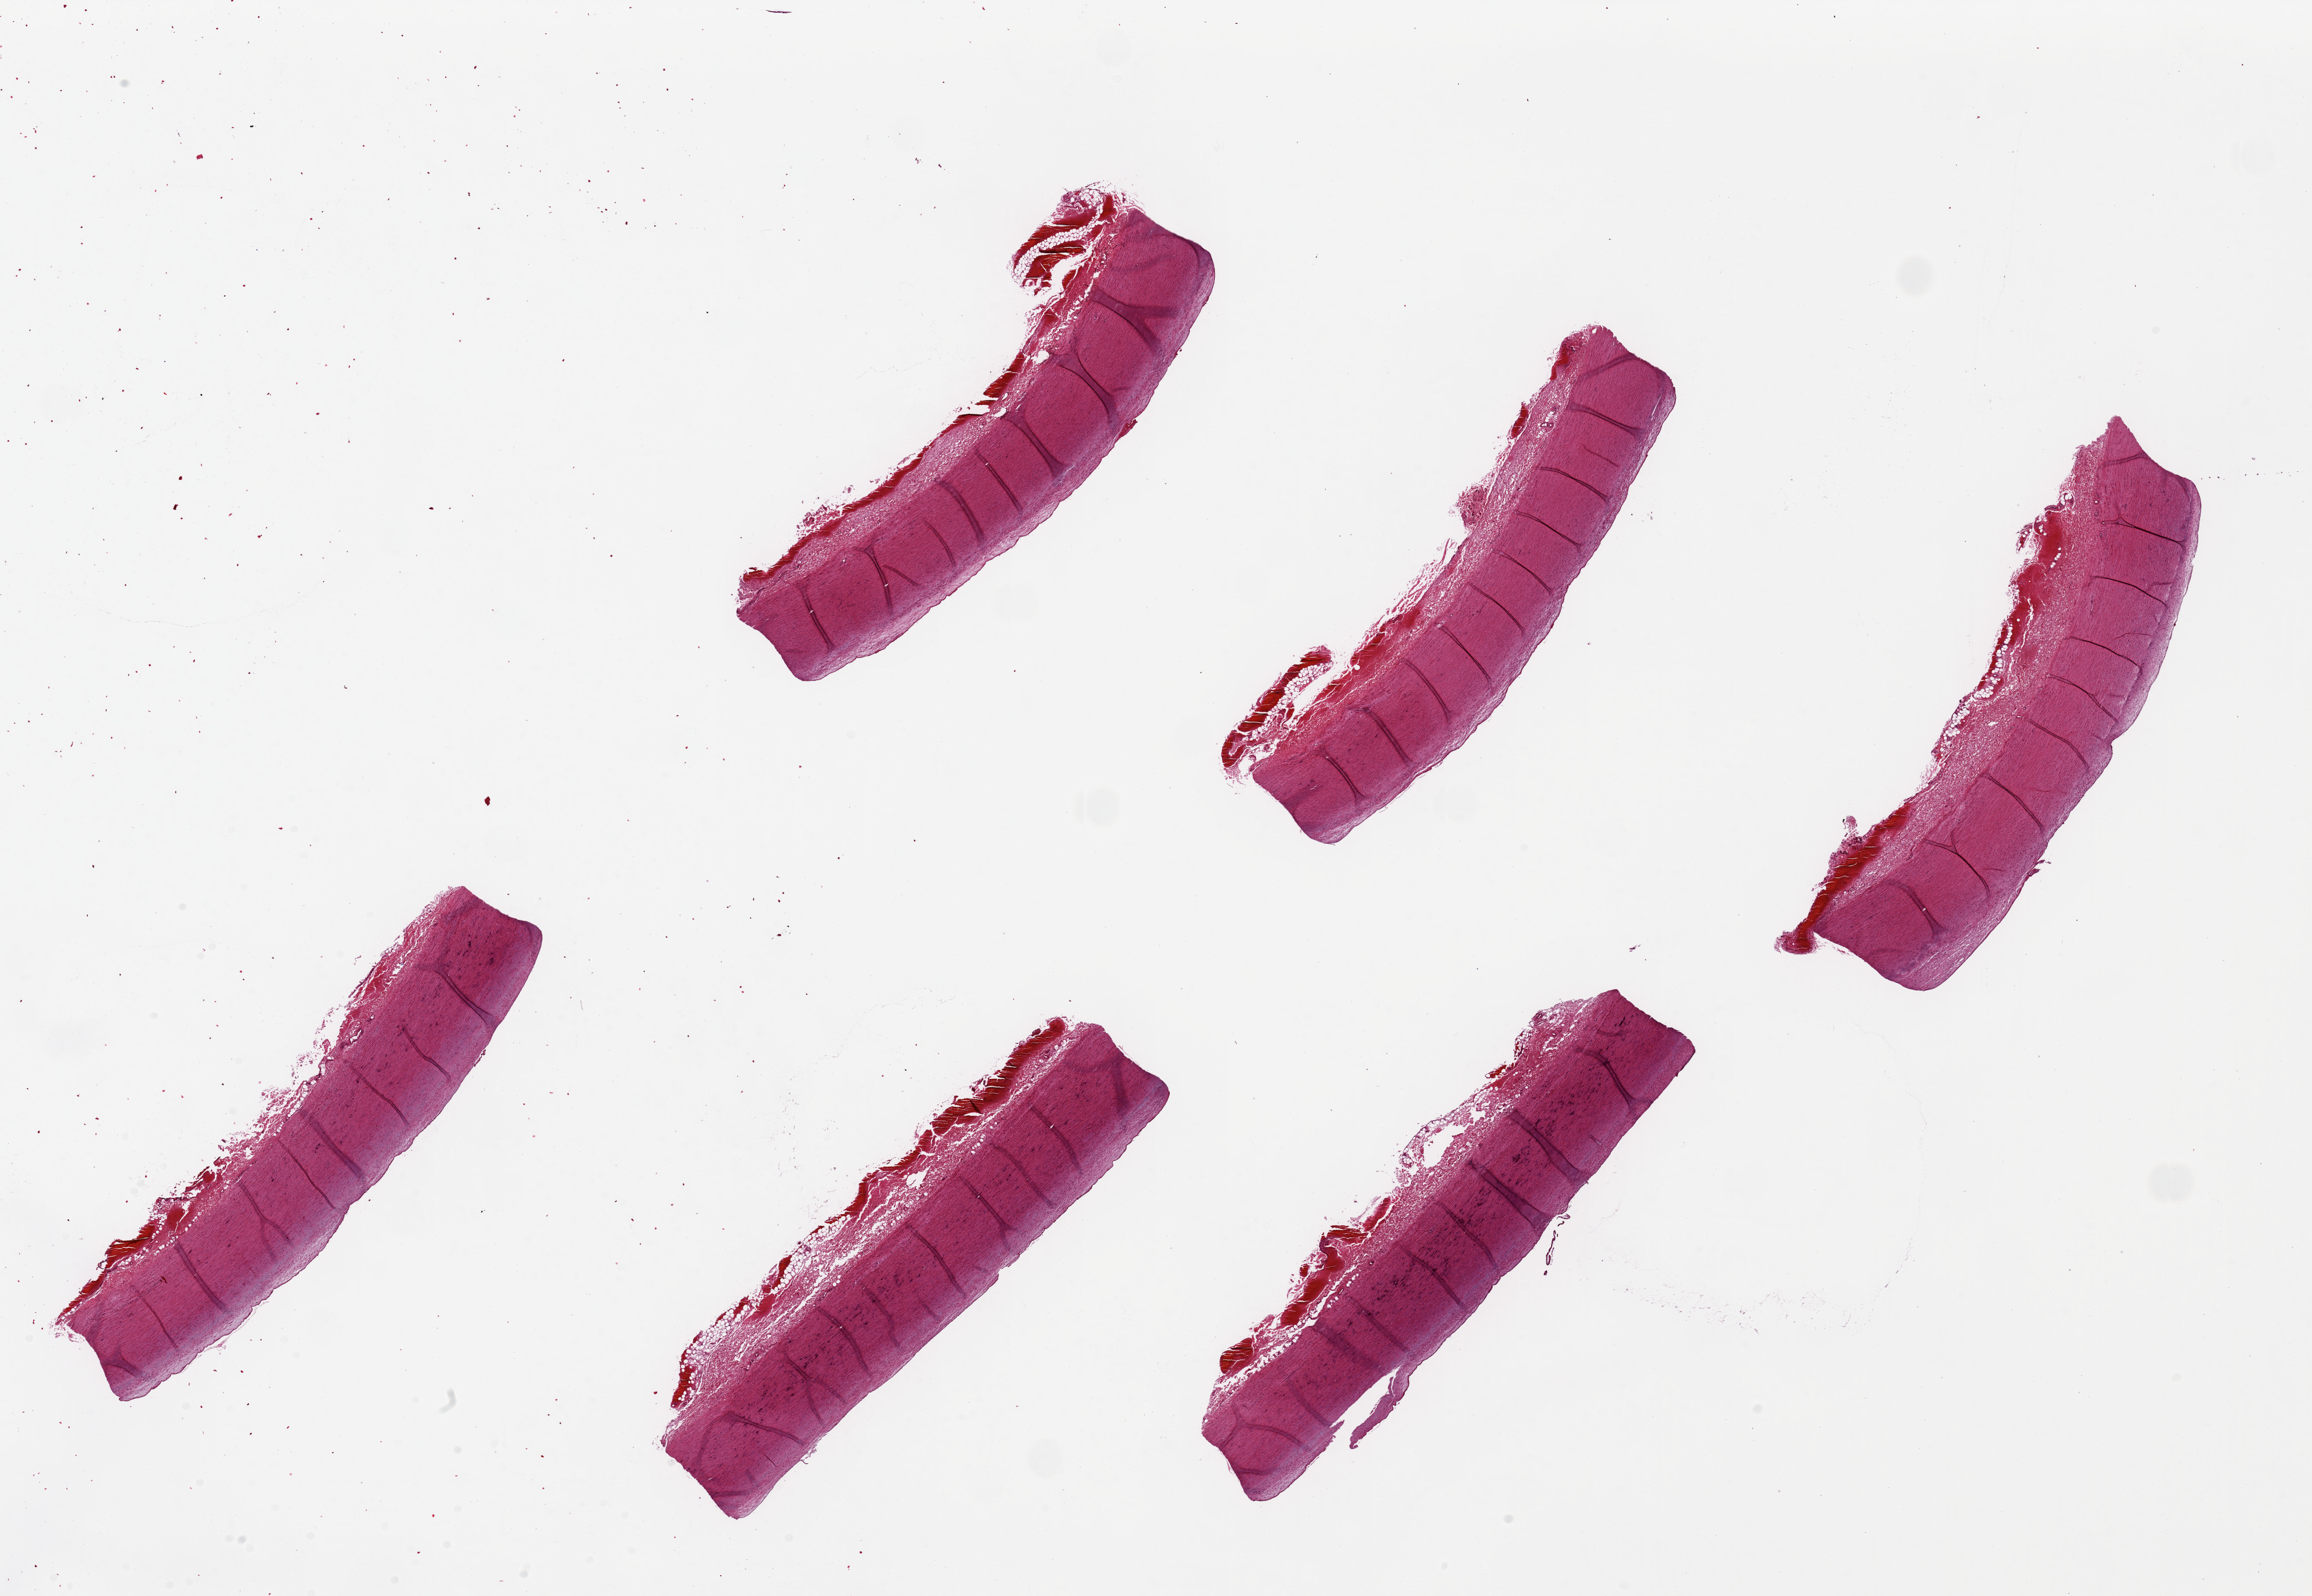
Whole-slide image, haematoxylin and eosin stain, low-resolution overview of the scanned area, about 31.5 x 21.7 mm (from a 20x scan), PAXgene-fixed, paraffin-embedded tissue, section of aorta (target tissue), tissue donor sample. Male donor.
• review note (as recorded): 6 pieces, up to 9x3mm